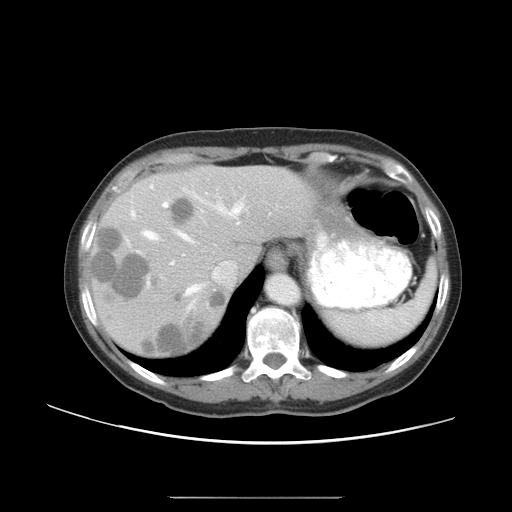
Contrast-enhanced abdominal CT, one axial slice. Position 37 of 50 along the scan axis. Reconstruction kernel STANDARD. 120 kVp. Soft-tissue window (W 400 / L 40 HU). 512 × 512 image matrix. Female patient, age 58 years. From the clinical record (not read from this slice): diagnosis: colorectal cancer liver metastases, imaged before liver resection; multiple liver metastases: yes; largest metastasis: 7.3 cm; chemotherapy before resection: yes.
Annotated regions visible in this slice (expert manual segmentation):
- hepatic veins: bounding box (x1, y1, x2, y2) in pixels: (131, 186, 244, 296)
- liver: (93, 166, 307, 358)
- planned liver remnant (the part of the liver to remain after resection): (180, 166, 306, 268)
- portal vein (with intrahepatic branches): (162, 192, 209, 264)
- liver metastasis: (141, 325, 209, 356)
- liver metastasis: (173, 197, 195, 226)
- liver metastasis: (211, 295, 225, 311)
- liver metastasis: (96, 228, 150, 299)